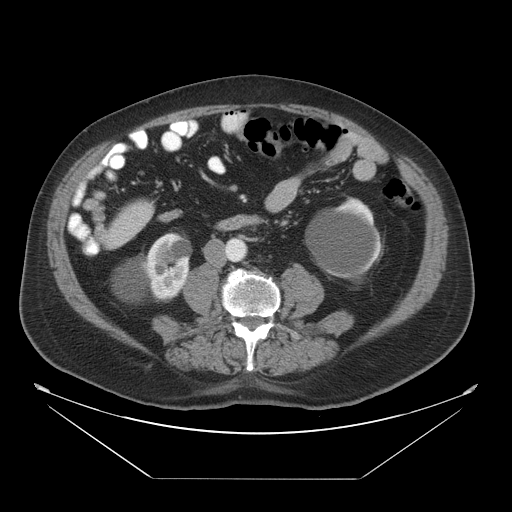
Contrast-enhanced abdominal CT, one axial slice. Slice 8 of 45 in the series (ordered by position). 120 kVp. Intravenous contrast given. Soft-tissue window (W 400 / L 40 HU). 5 mm slice thickness. 512 × 512 image matrix, field of view 463 × 463 mm. Male patient, age 87 years. Case-level facts recorded for this patient, not image findings: diagnosis: colorectal cancer liver metastases, imaged before liver resection; multiple liver metastases: no; largest metastasis: 4.5 cm; disease in both lobes: yes.
Annotated regions visible in this slice (outlined manually by an expert reader):
- liver: box from (x=106, y=201) to (x=155, y=249) px